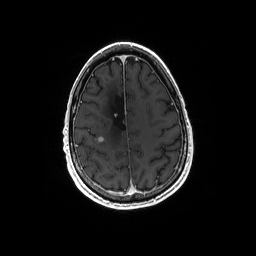
Brain MRI from a brain-tumour surgery series, one axial slice. Slice 51 of 192 in the series (ordered by position). T1-weighted post-contrast. 256 × 256 image matrix, field of view 256 × 256 mm. Case-level facts recorded for this patient, not image findings: histopathology: Astrocytoma; WHO grade: 4; IDH mutation: yes.
Outlined on this slice (manually delineated by an expert):
- tumour: bounding box (x1, y1, x2, y2) in pixels: (95, 139, 104, 144)